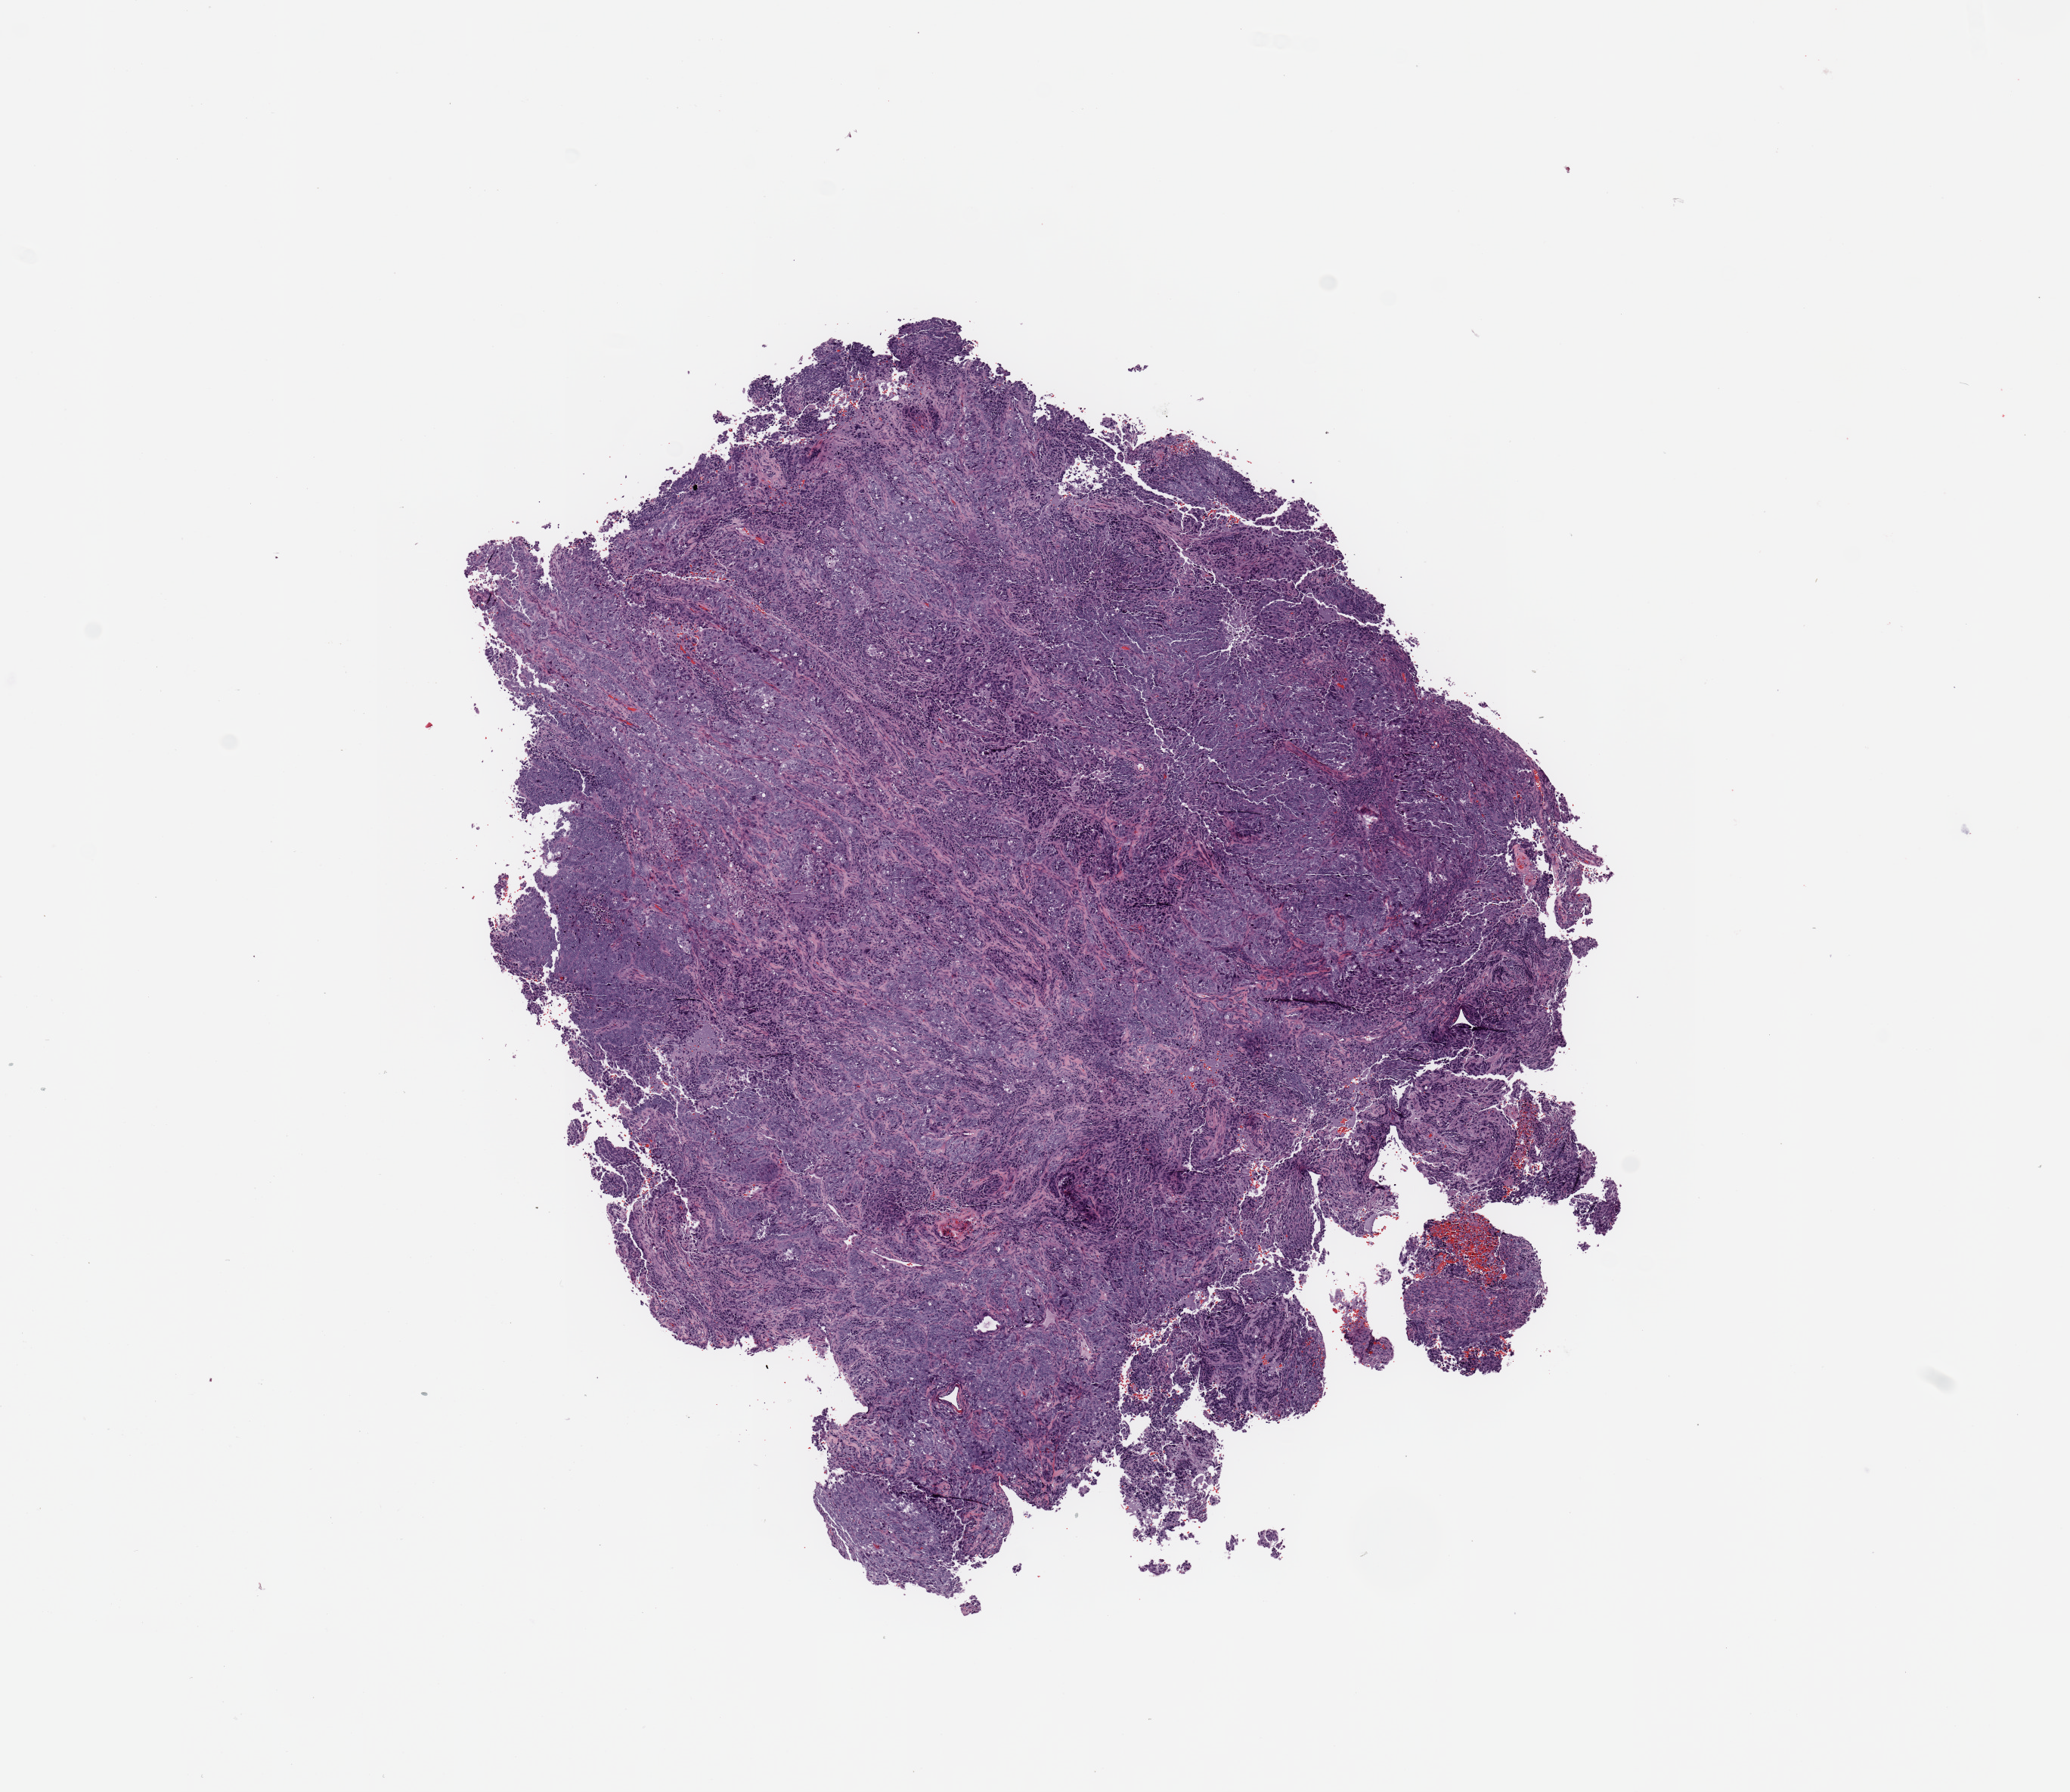
Whole-slide histology image, H&E-stained, low-resolution overview of the scanned area, about 10.8 x 9.4 mm, tumour tissue sample, sampled site: uterus. Female, 68 y/o. Histologic grade: G3 (poorly differentiated). Pathologist review of this section (percent, as recorded): tumour nuclei 95%, necrosis 0%.
AJCC pathologic stage: III. Diagnosis: Endometrioid adenocarcinoma, NOS.